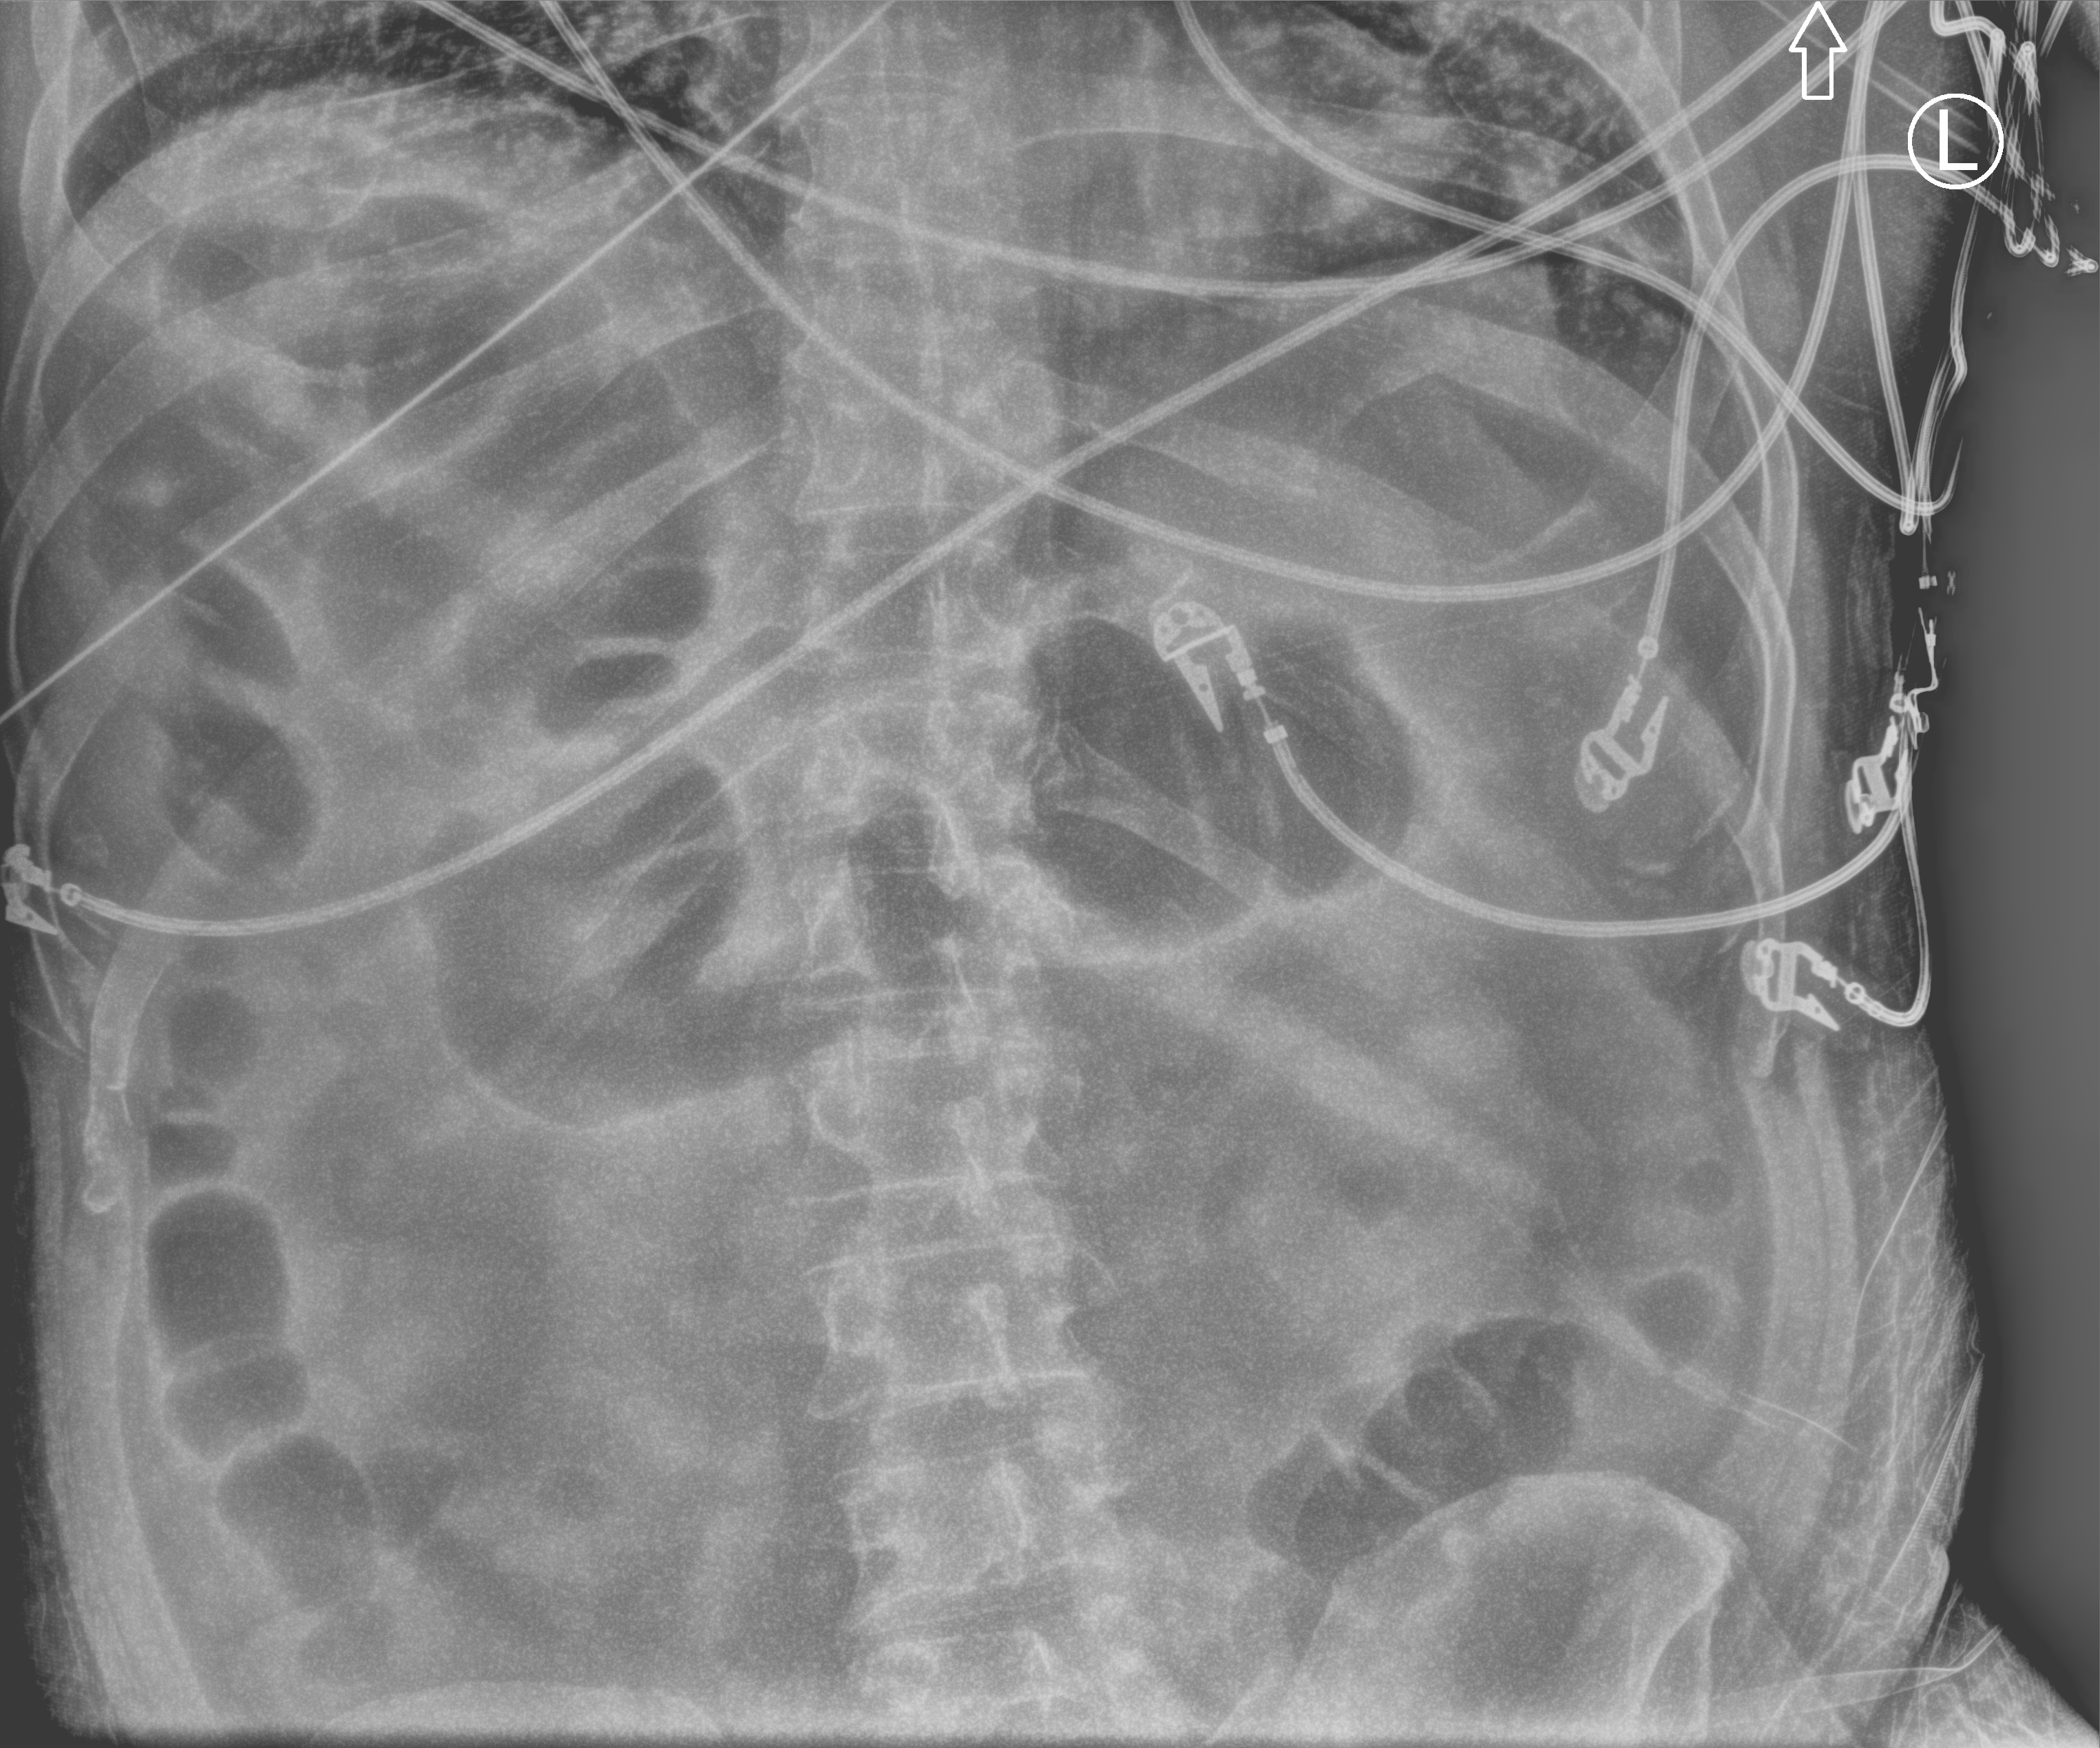
Portable abdomen radiograph, anteroposterior (AP) projection. Patient hospitalised with COVID-19; male, aged 18–59 years.
From the hospital-stay record, not from the radiograph (when in the stay this image was taken is not recorded):
- admitted to intensive care during this hospital stay: yes
- COPD (admission record): no